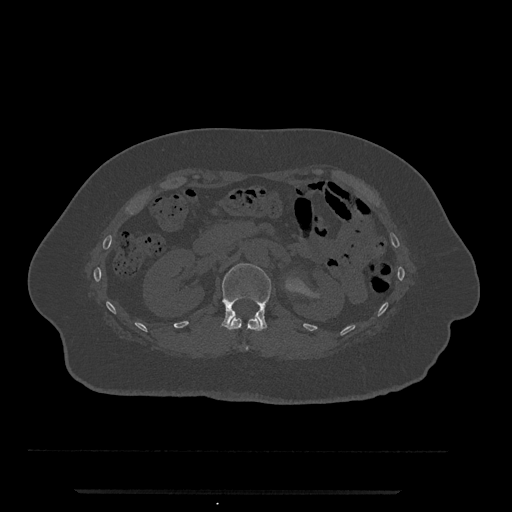
CT including the spine, one axial slice. Slice 127 of 797 in the series (ordered by position). Bone window (W 1800 / L 400 HU). 512 × 512 image matrix, field of view 440 × 440 mm. Patient: female, 51 years. Case-level facts recorded for this patient, not image findings: primary cancer: neuro; vertebrae with lytic lesions (as recorded): T8.
Structures marked on this image (semi-automatic segmentation, software-assisted and operator-edited):
- L1 vertebra: box from (x=221, y=263) to (x=271, y=329) px
- T12 vertebra: (x=227, y=317)–(x=263, y=351)